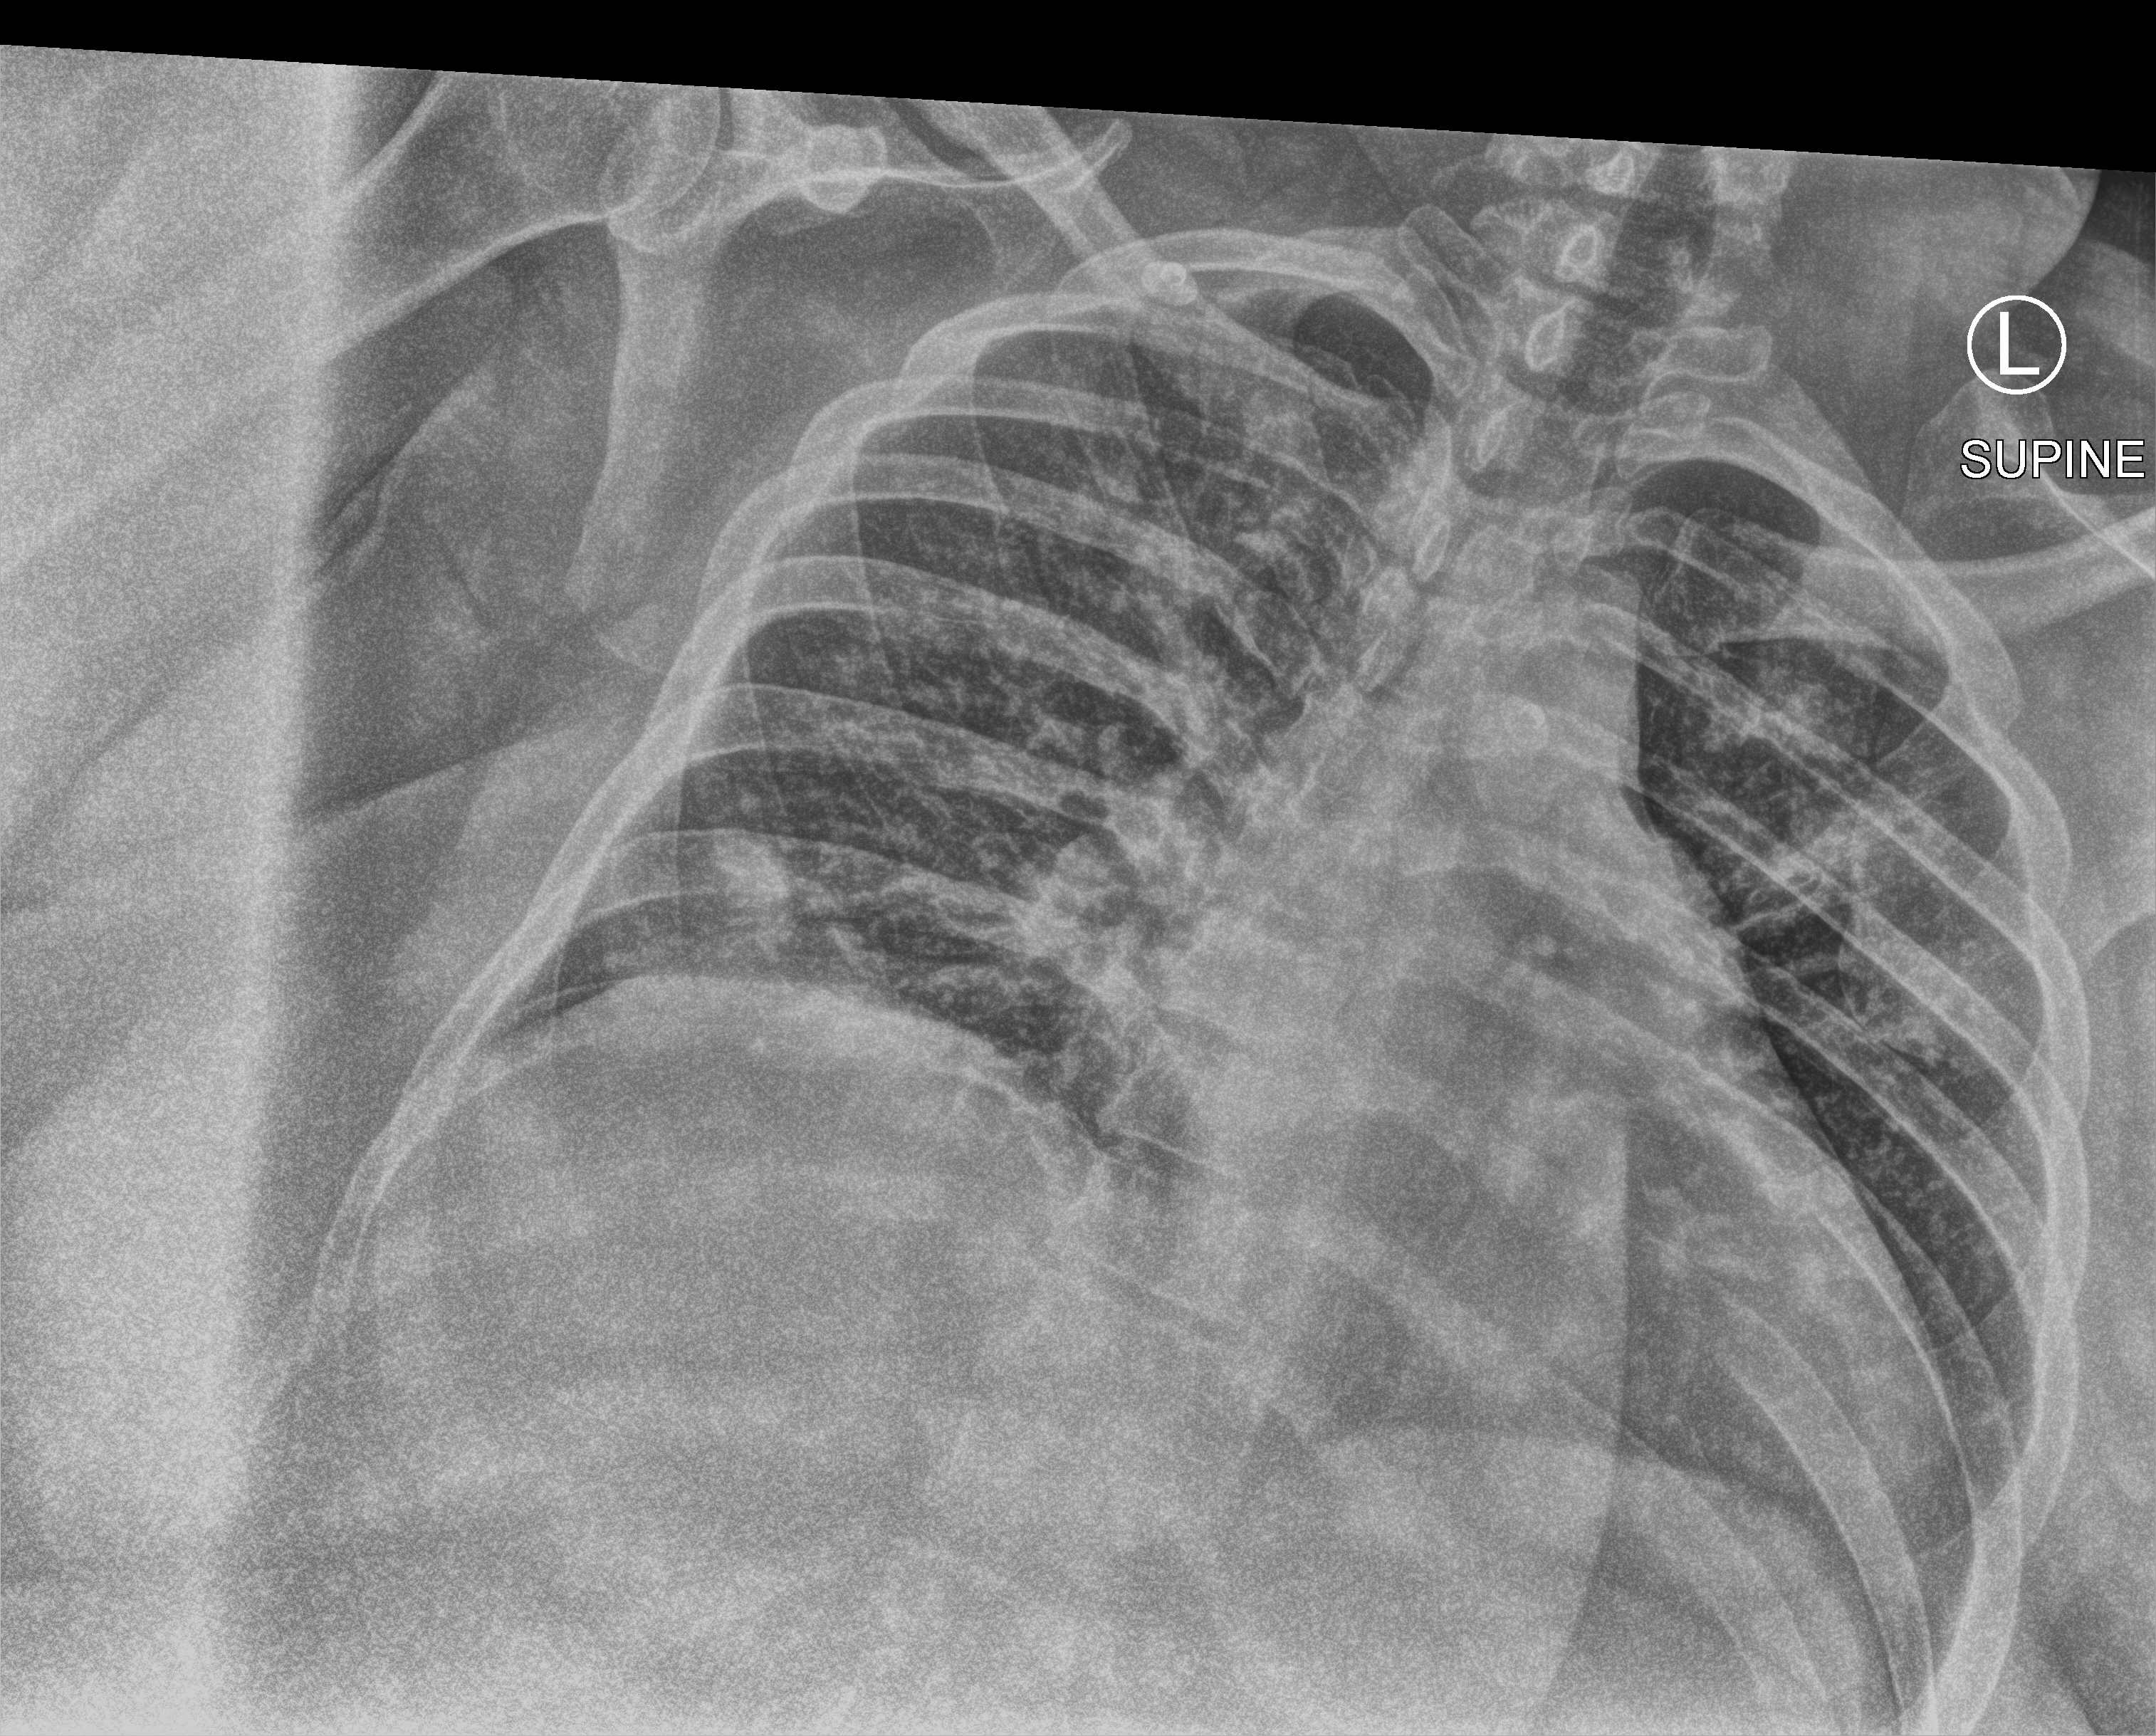
Bedside chest radiograph (computed radiography); anteroposterior (AP) projection. Female patient hospitalised with COVID-19, age 18–59 years.
Admission-level facts for this patient (not findings on this image; timing relative to this image not recorded):
- hypertension (admission record): yes
- other chronic lung disease (admission record): no